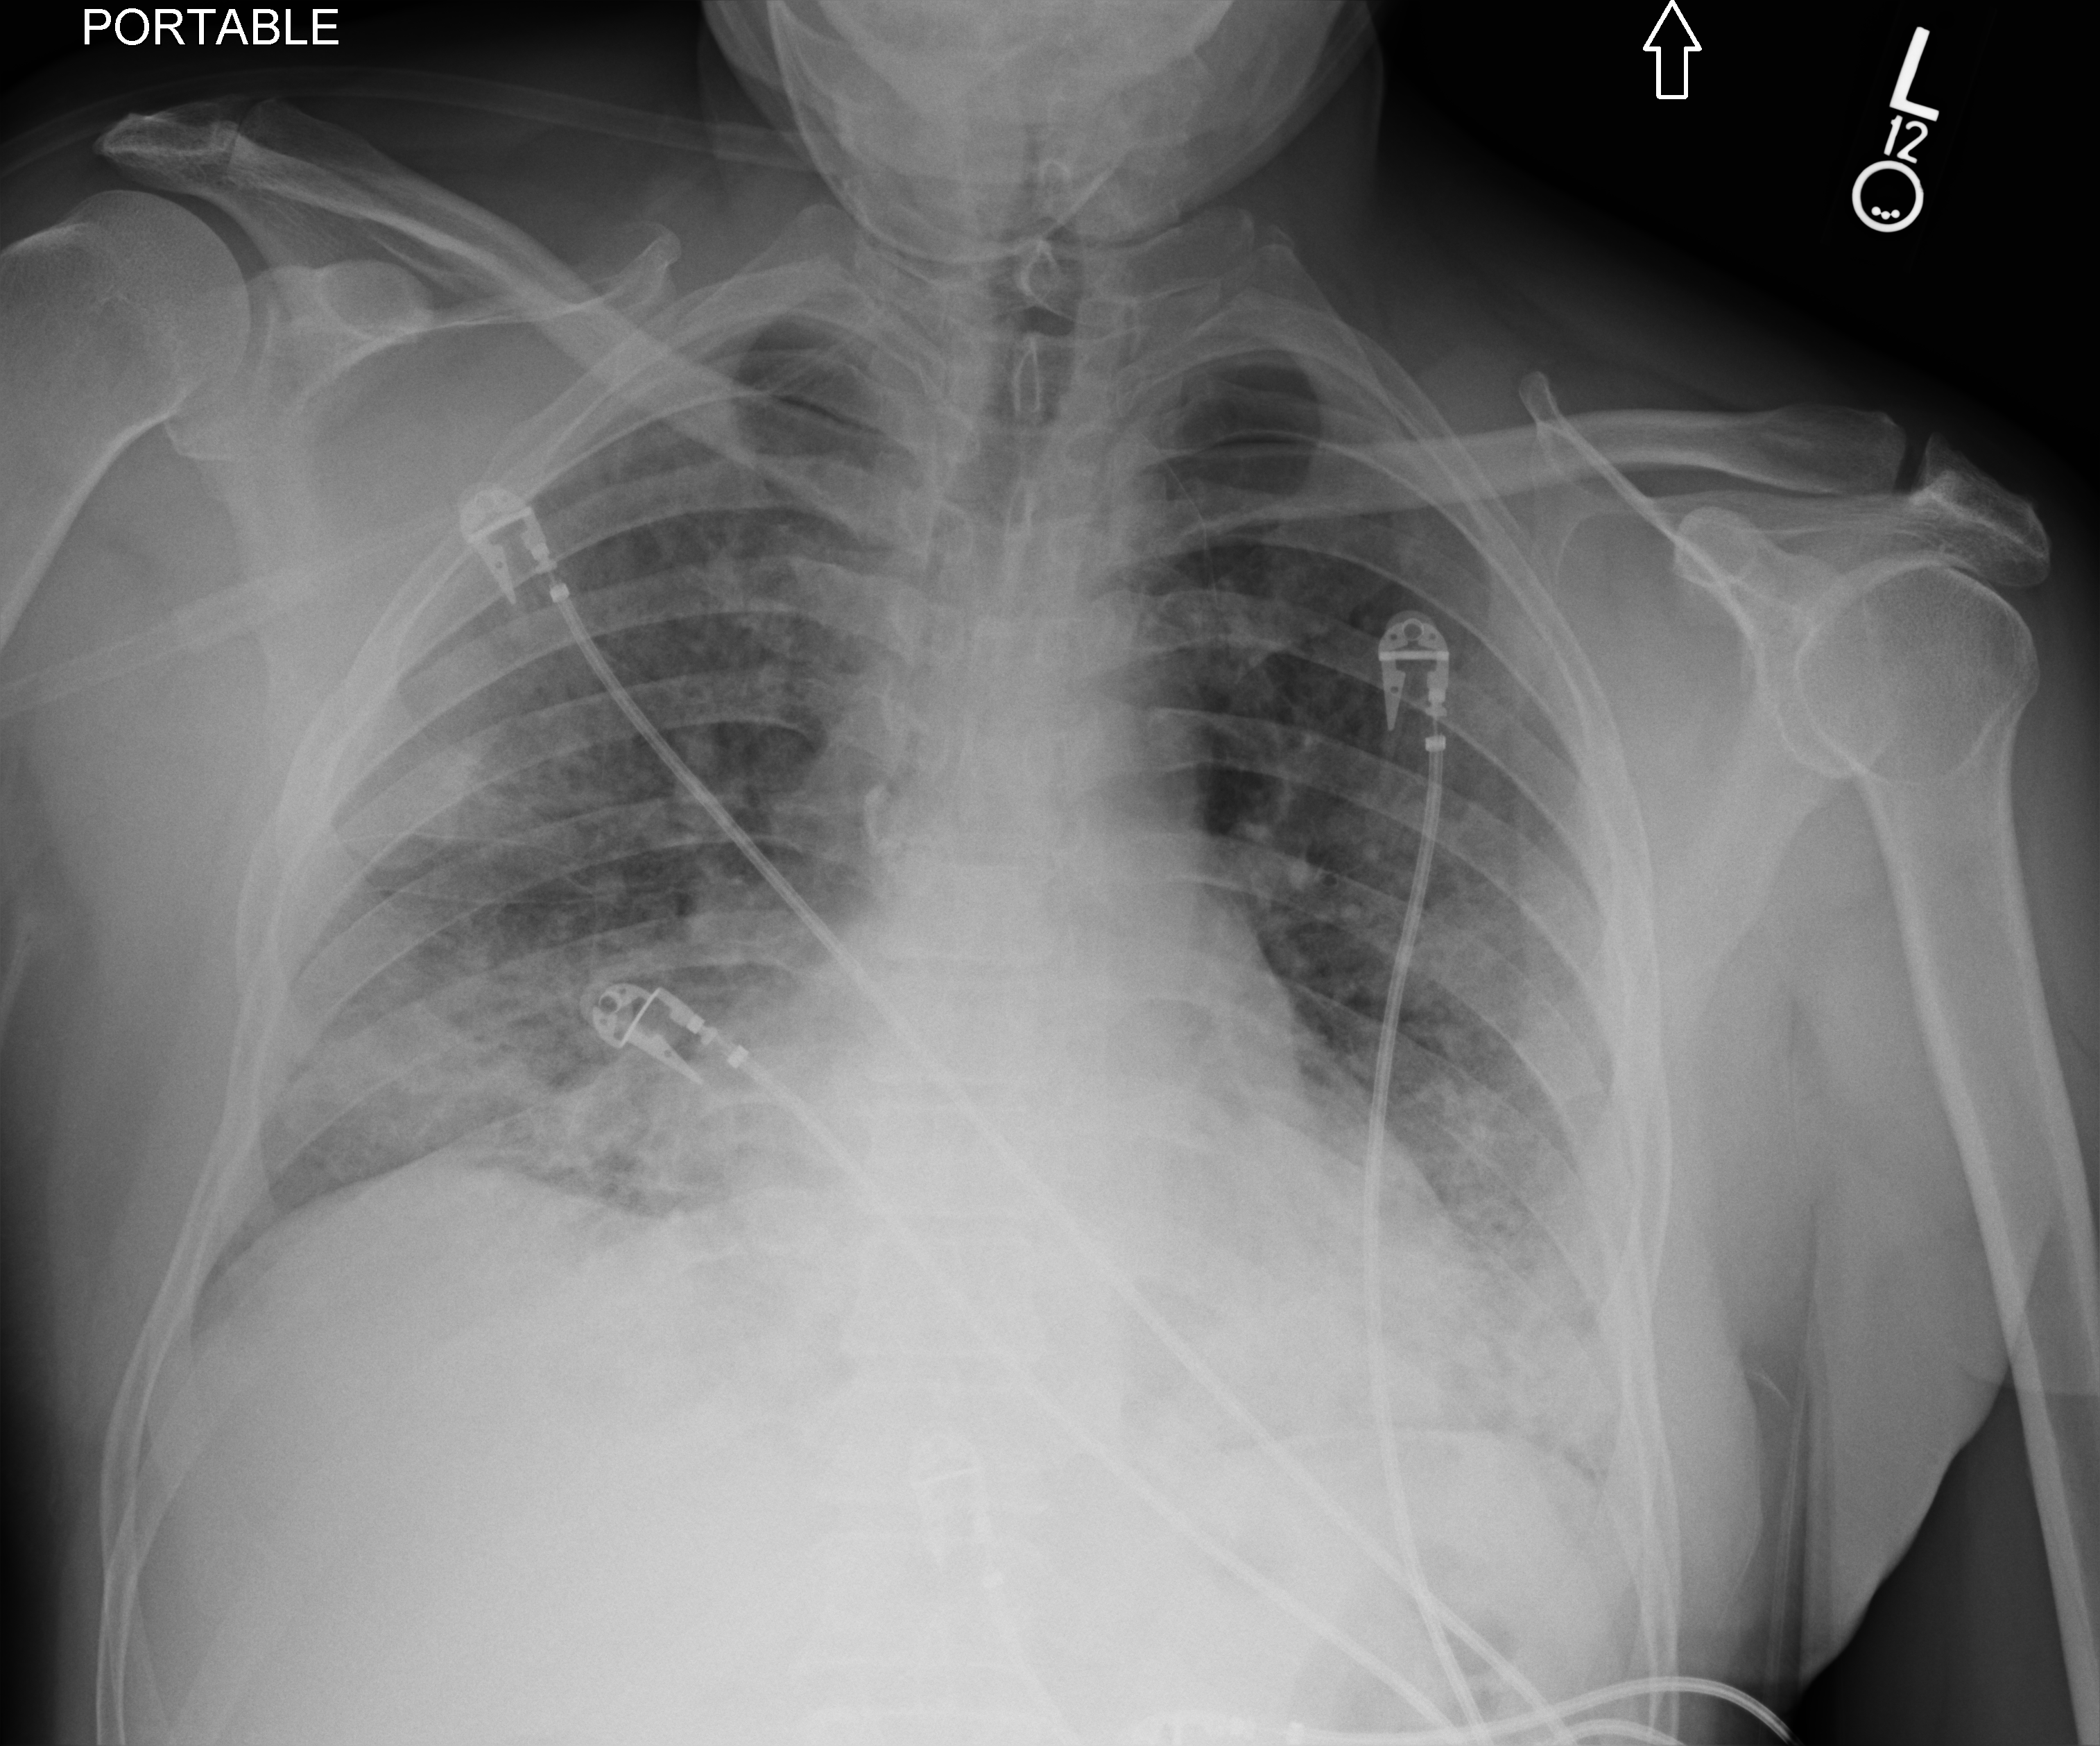
Chest X-ray (portable), anteroposterior (AP) projection. Male patient hospitalised with COVID-19, age 18–59 years.
Hospital-stay facts (about this admission, not read from this image; timing relative to this image not recorded): mechanically ventilated during this hospital stay: no; admitted to intensive care during this hospital stay: yes.